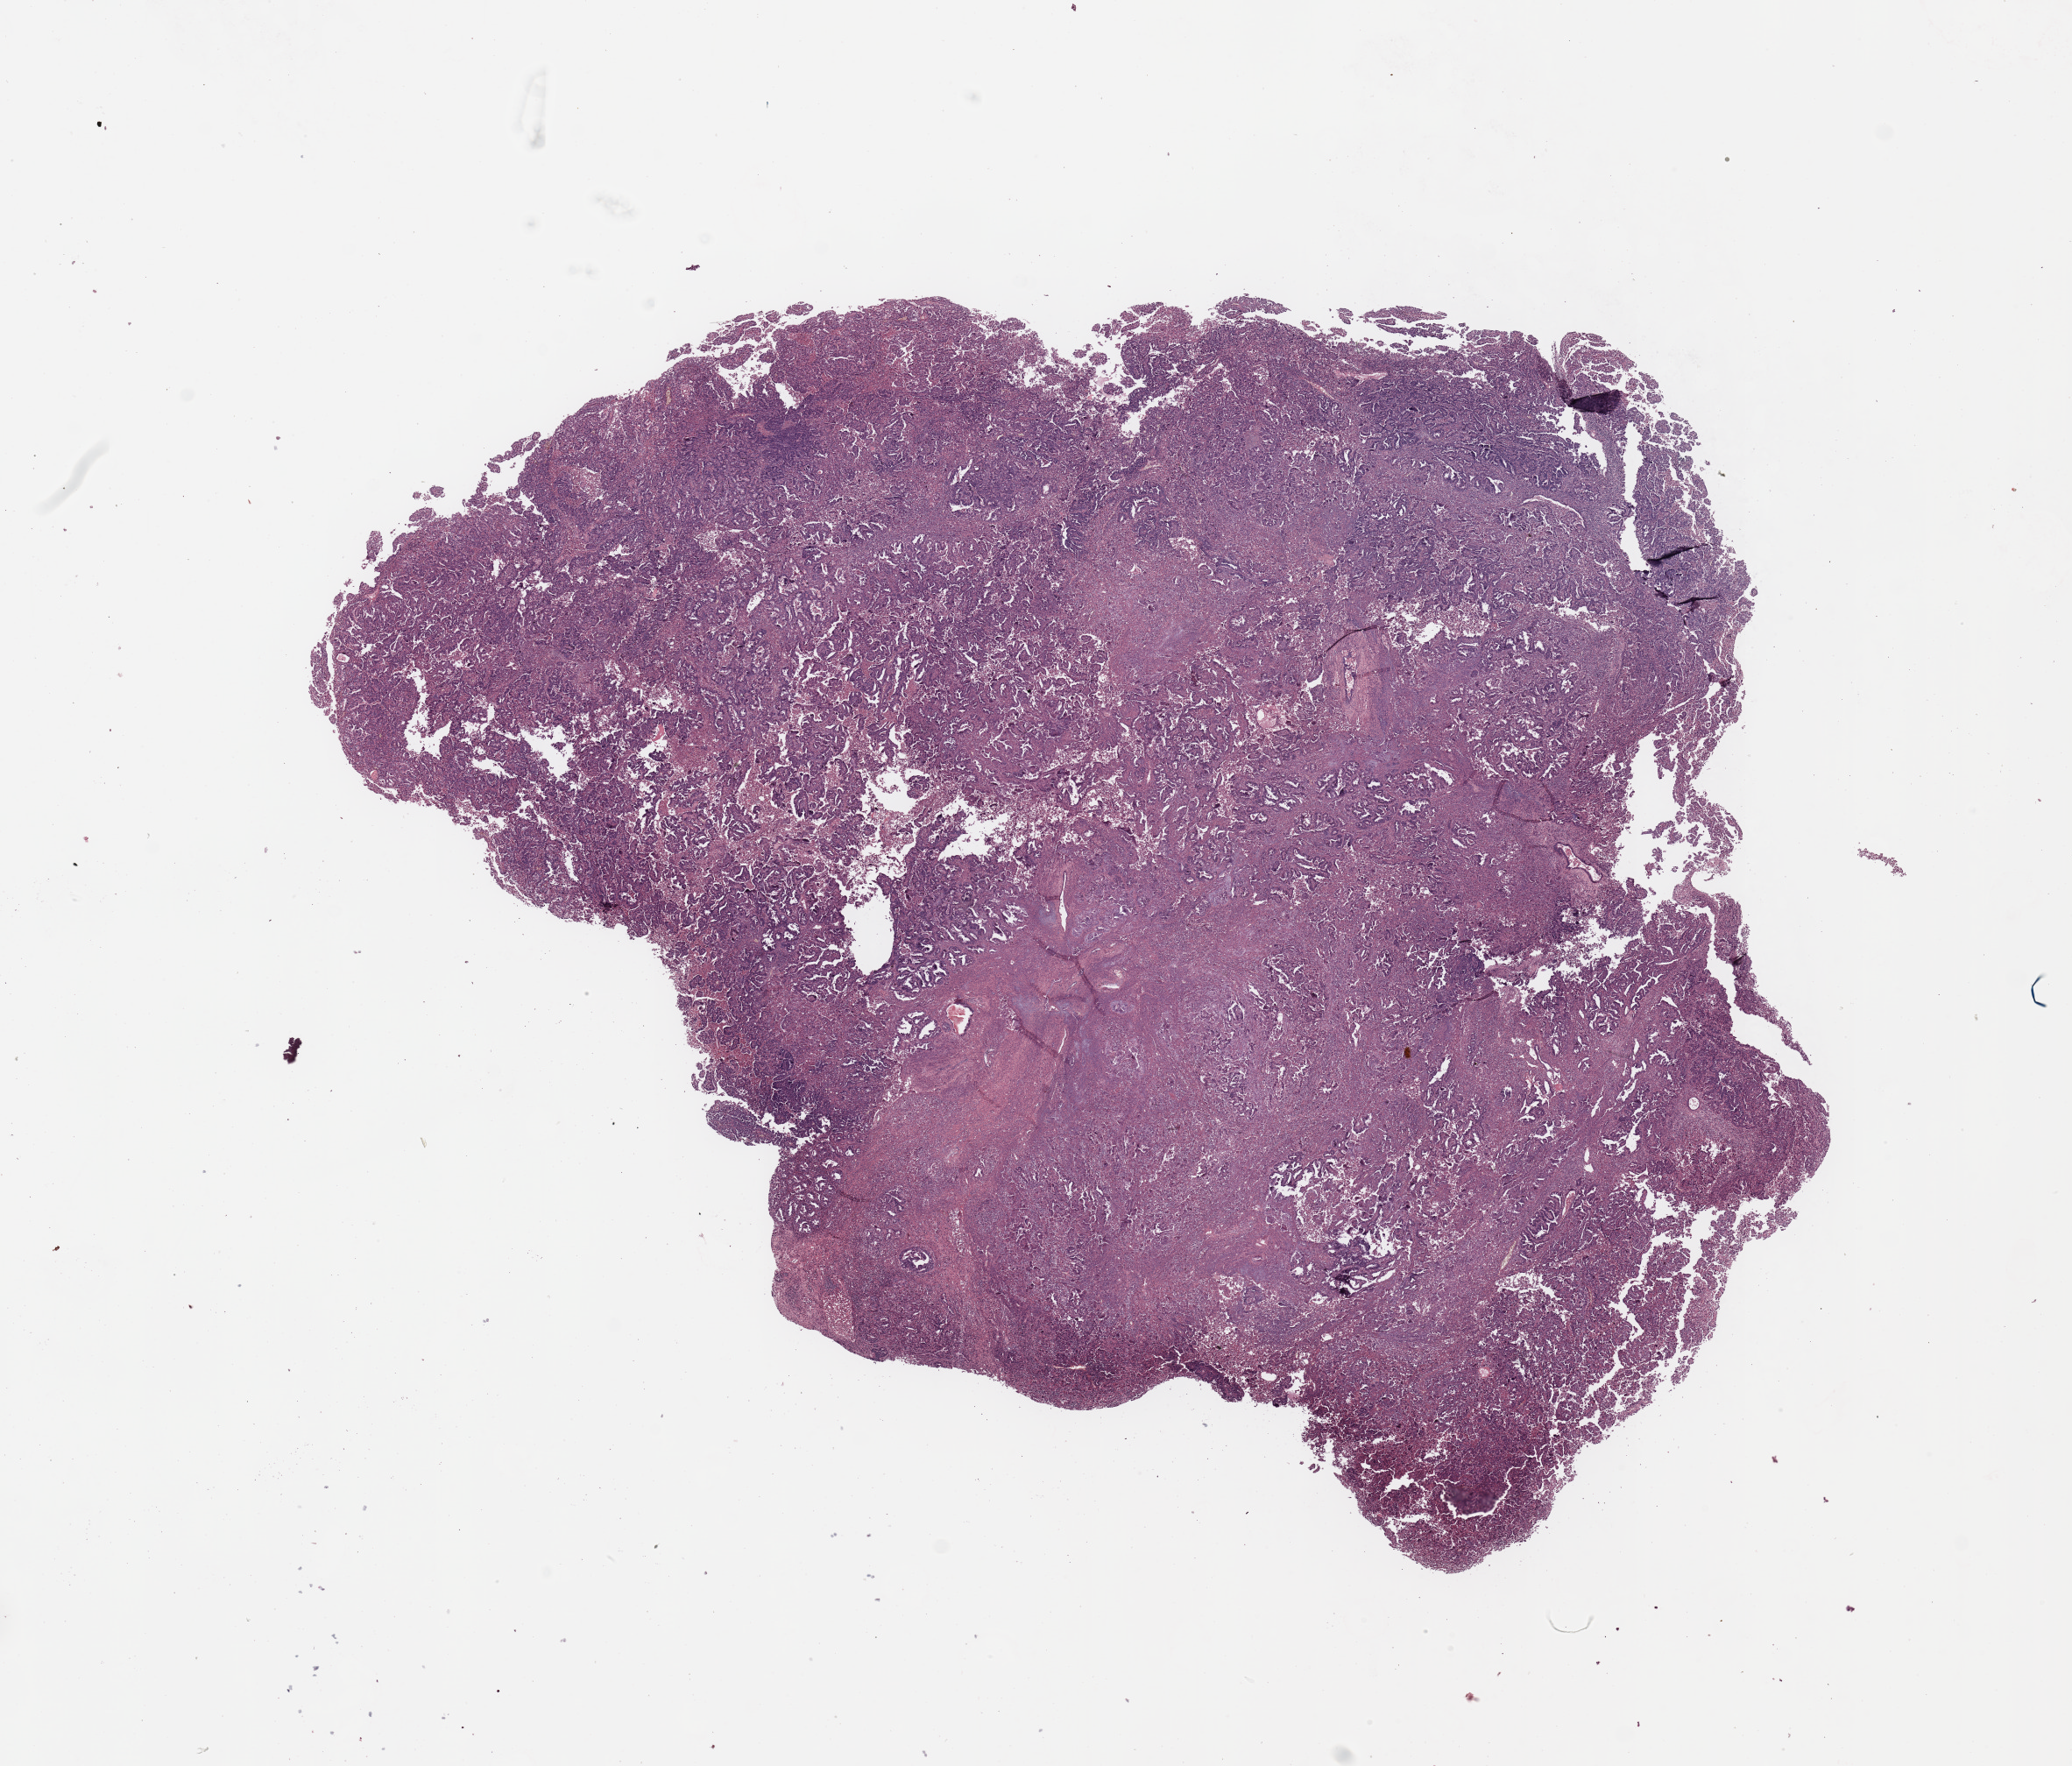
Digitized H&E-stained tissue section (whole slide), a low-resolution overview of the entire scanned area, about 18.7 x 15.9 mm (from a 20x scan). Tumour tissue sample, sampled site: uterus. Patient: female, age 74 years. Histologic grade: G3 (poorly differentiated). Composition of this section per pathologist review: tumour nuclei 90%, necrosis 5%.
- histologic diagnosis: Endometrioid adenocarcinoma, NOS
- AJCC pathologic stage: II